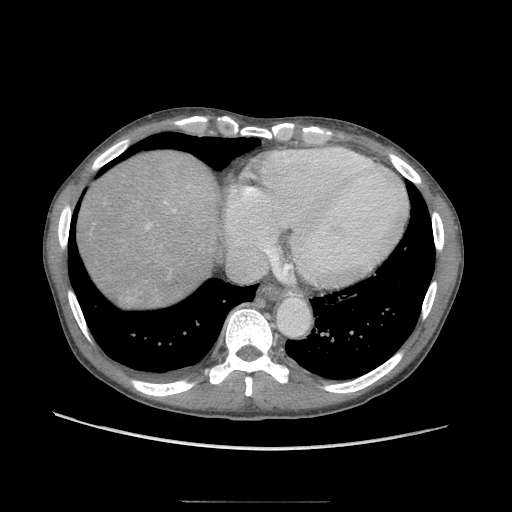
Contrast-enhanced abdominal CT (liver protocol), one axial slice. Reconstruction kernel STANDARD. 120 kVp. Soft-tissue window (W 400 / L 40 HU). 2.5 mm slice thickness. 512 × 512 image matrix. From the clinical record (not read from this slice): diagnosis: hepatocellular carcinoma (patient treated with transarterial chemoembolisation; whether this scan precedes or follows treatment is not stated here); TNM stage (as recorded): Stage-IIIA; Child-Pugh class: A.
Structures marked on this image (semi-automatically segmented with operator editing):
- abdominal aorta: bounding box [x1, y1, x2, y2] px = [277, 298, 309, 334]
- liver parenchyma outside the tumour (the mass and vessels are separate outlines, so this box may not span the whole liver): [78, 150, 216, 300]